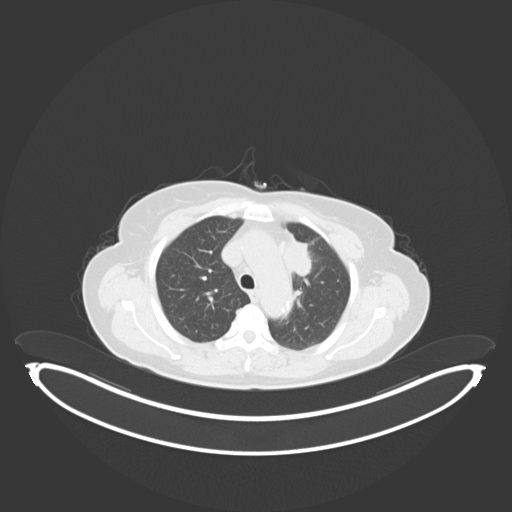
Chest CT, one axial slice; position 194 of 243 along the scan axis; reconstruction kernel B30f; 120 kVp; lung window (W 1500 / L -600 HU); 3 mm slice thickness; 512 × 512 image matrix, field of view 500 × 500 mm. Patient: female, 65 years. Case-level facts recorded for this patient, not image findings: clinical TNM (as recorded): T2a N0 M0.
Outlined on this slice (rectangle marked by the reading radiologist):
- lung tumour (recorded histology: adenocarcinoma): bounding box [x1, y1, x2, y2] px = [281, 231, 313, 281]